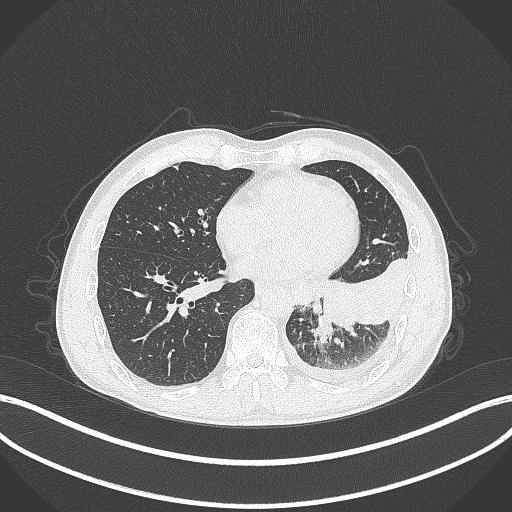
Chest CT, one axial slice. Slice 108 of 295 in the series (ordered by position). Reconstruction kernel B70f. 120 kVp. Lung window (W 1500 / L -600 HU). 1 mm slice thickness. 512 × 512 image matrix, field of view 400 × 400 mm. Patient: male, 47 years. From the clinical record (not read from this slice): clinical TNM (as recorded): T3 N1 M1c.
Outlined on this slice (bounding box drawn by a radiologist):
- lung tumour (recorded histology: small cell carcinoma): box from (x=310, y=316) to (x=332, y=344) px